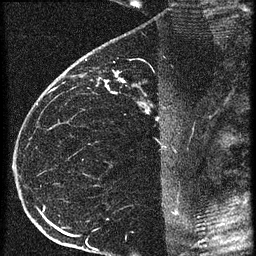
Breast MRI (dynamic contrast-enhanced), one sagittal slice. Position 39 of 60 along the scan axis. 3 images stored at this slice position (order not interpretable as contrast timing). 1.5 T. TE 4.2 ms, TR 20.4 ms. 1.5 mm slice thickness. 256 × 256 image matrix, field of view 180 × 180 mm. Female patient, age 35 years. Case-level facts recorded for this patient, not image findings: setting: breast cancer imaged before/during neoadjuvant chemotherapy; receptor status: HR-positive, HER2-negative.
Annotated regions visible in this slice (semi-automatically segmented with operator editing):
- analysis volume of interest (the breast-tissue region the enhancement analysis was run in; not a lesion): bounding box <65,60,169,119> (left, top, right, bottom; pixels)
- tumour enhancement mask (voxels above the 90 % enhancement threshold inside the analysis volume of interest): <99,74,148,111>